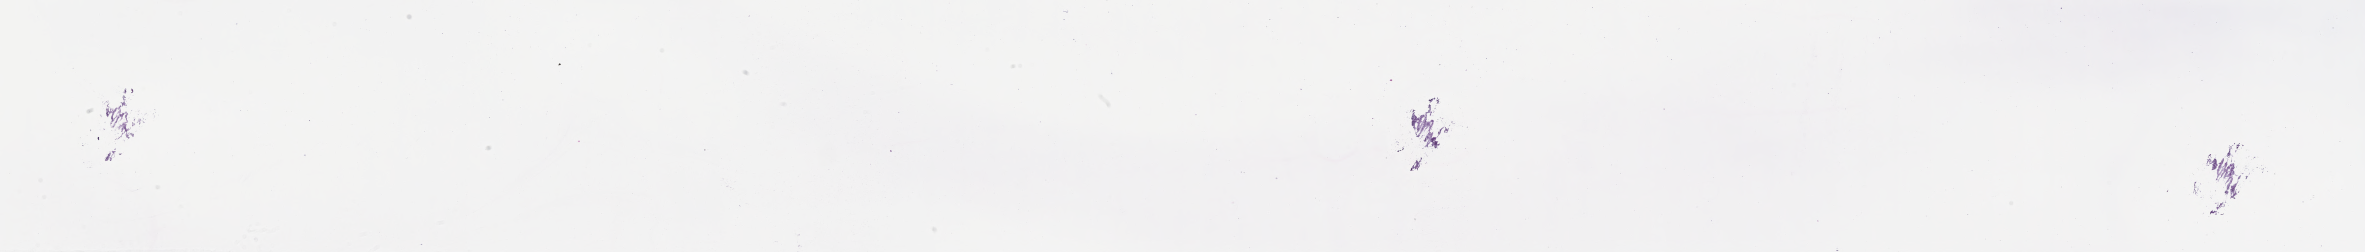
Whole-slide image, haematoxylin and eosin stain of tumor tissue from the brain, whole scanned area (about 38.2 x 4.1 mm) shown as a low-resolution overview. Frozen section. Male patient, age 72 months.
Recorded diagnosis: Neoplasm, uncertain whether benign or malignant.